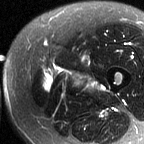
MRI of an extremity soft-tissue mass, one axial slice; position 14 of 60 along the scan axis; T2-weighted fat-saturated; MR volume resampled by the dataset authors to the PET/CT grid (not the native acquisition matrix); 3.27 mm slice thickness; 144 × 144 image matrix, field of view 141 × 141 mm. Female patient. From the clinical record (not read from this slice): histological type: pleiomorphic leiomyosarcoma; grade: intermediate; site of the primary tumour: left thigh.
Outlined on this slice (expert contour drawn on MRI and transferred to this co-registered scan by the dataset authors):
- gross tumour volume including surrounding oedema: bounding box [x1, y1, x2, y2] px = [43, 69, 103, 93]